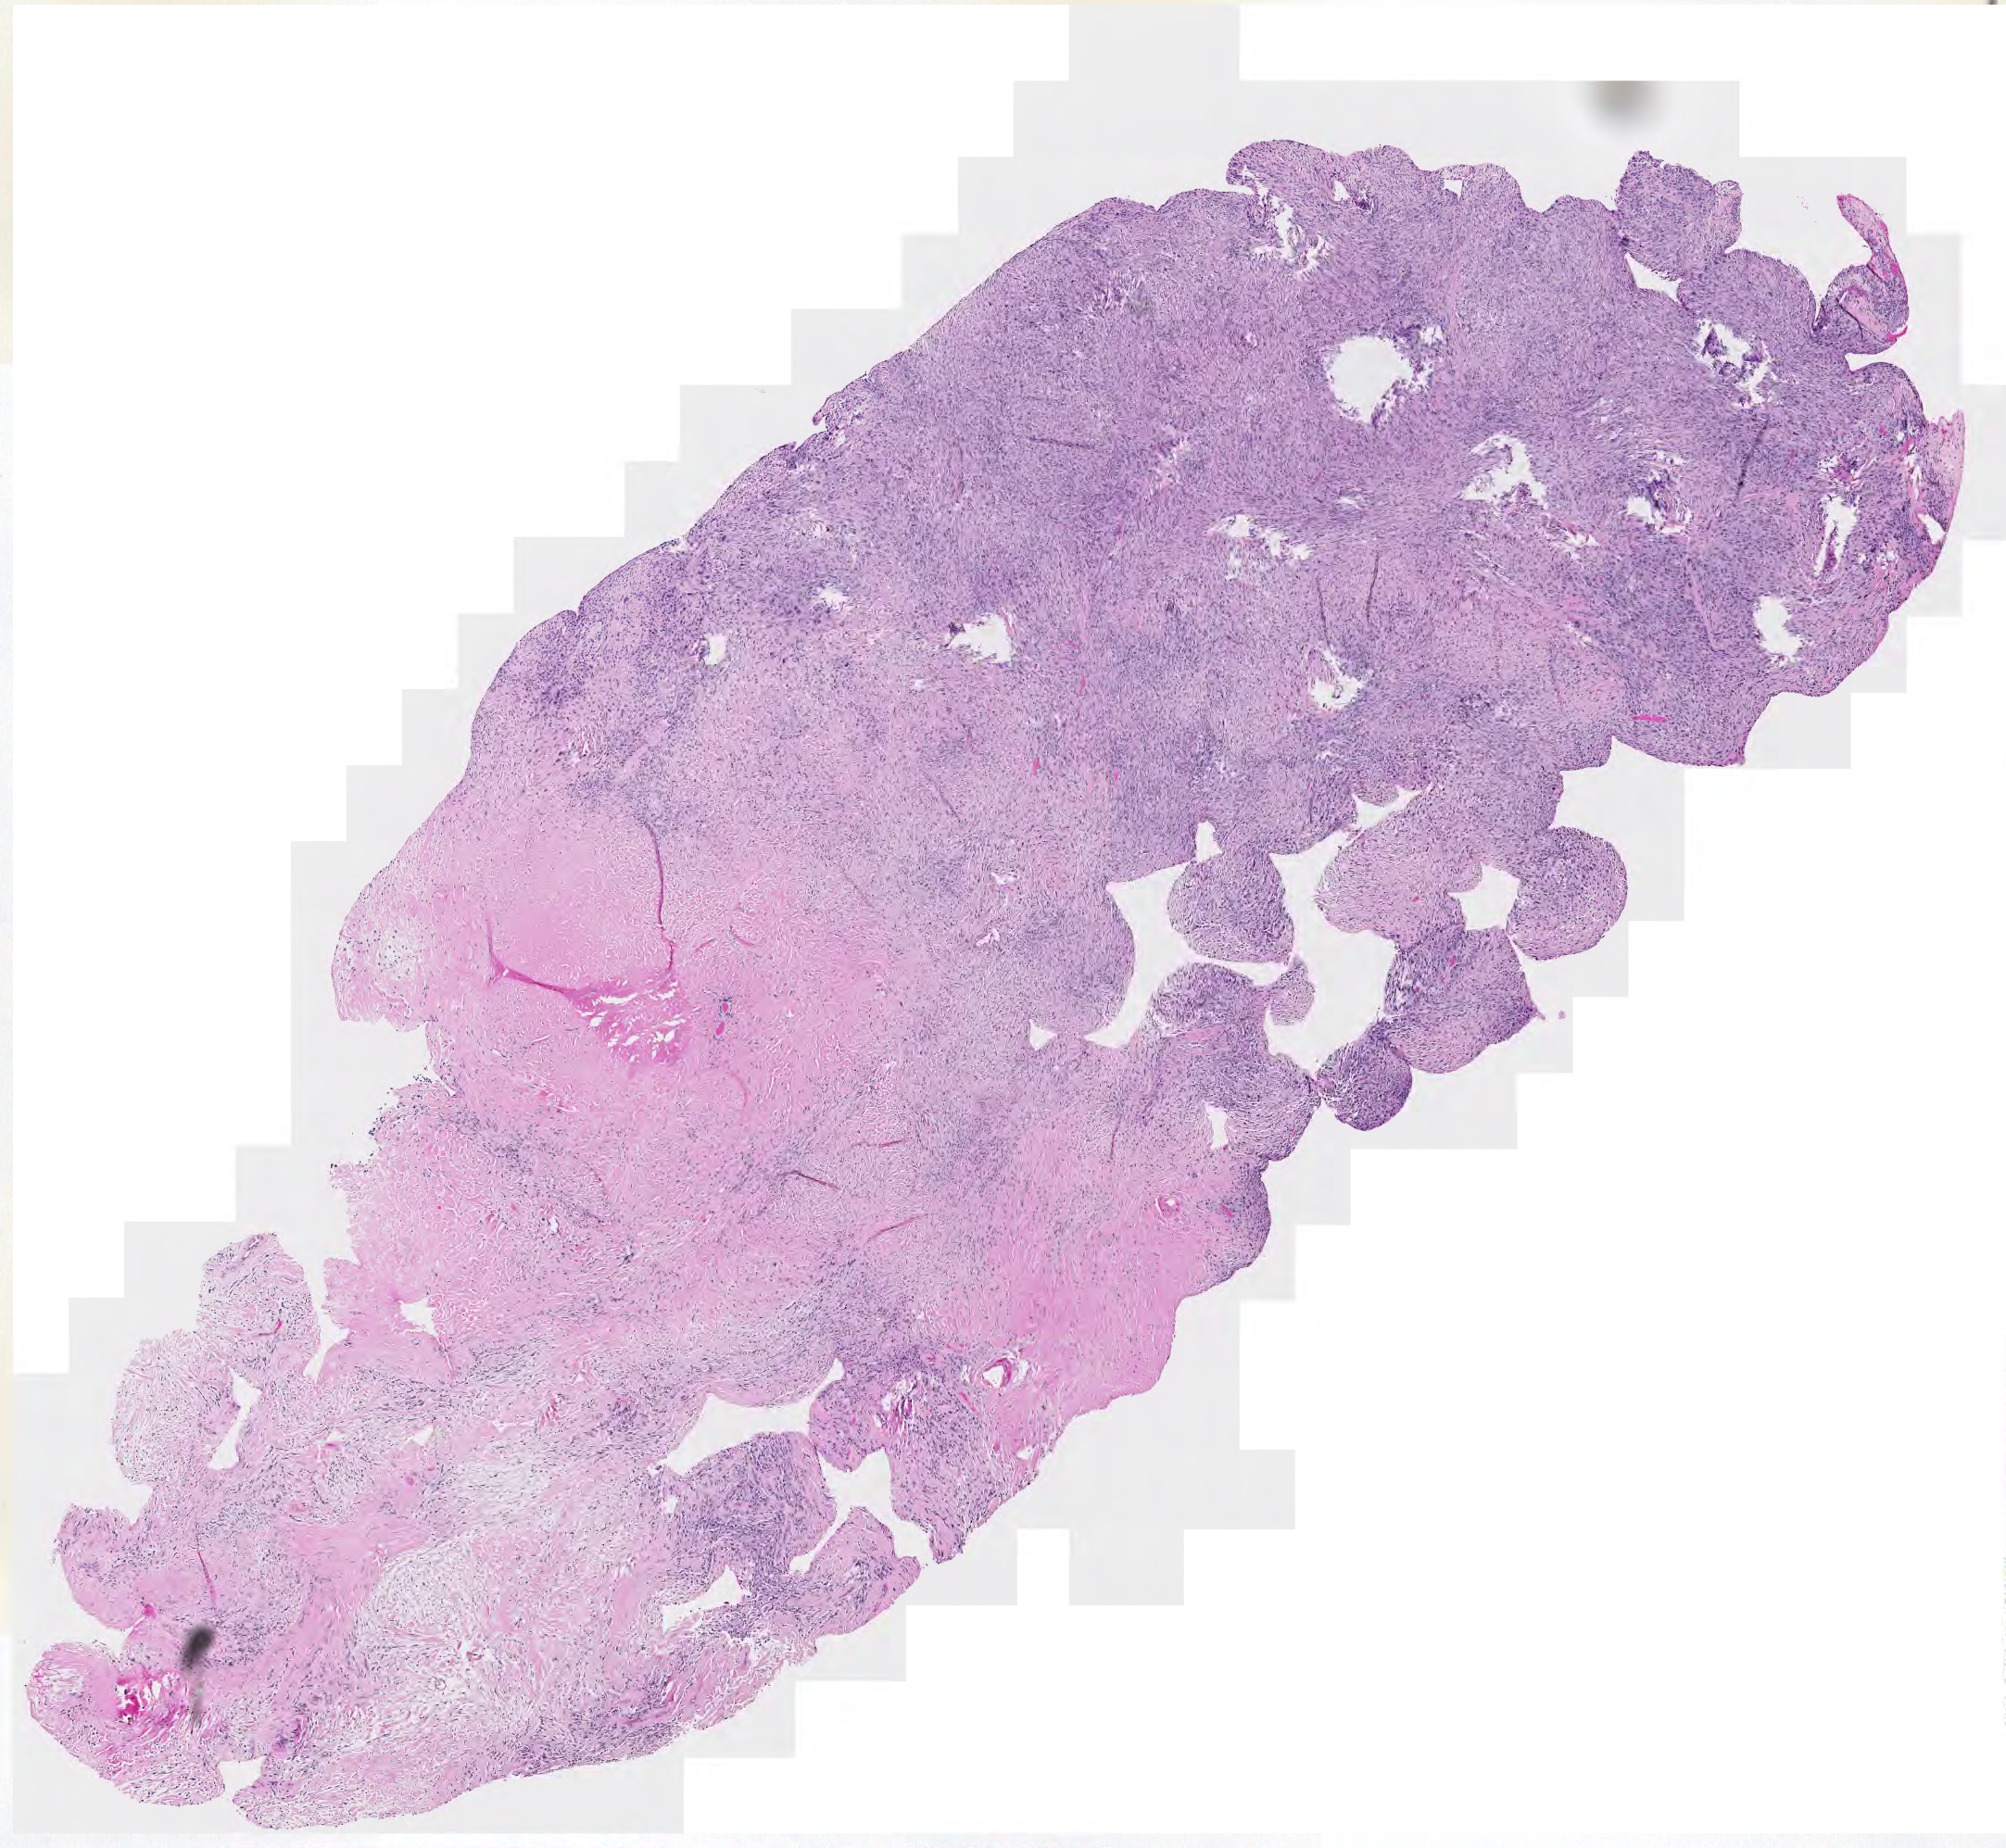
Digitized H&E tissue section (whole slide) — low-resolution overview of the scanned area, about 11.2 x 10.3 mm (acquisition: 20x scan), tumour tissue sample. 81-year-old male patient.
Patient diagnosis (cohort enrolment): sarcoma (site not recorded at cohort level).